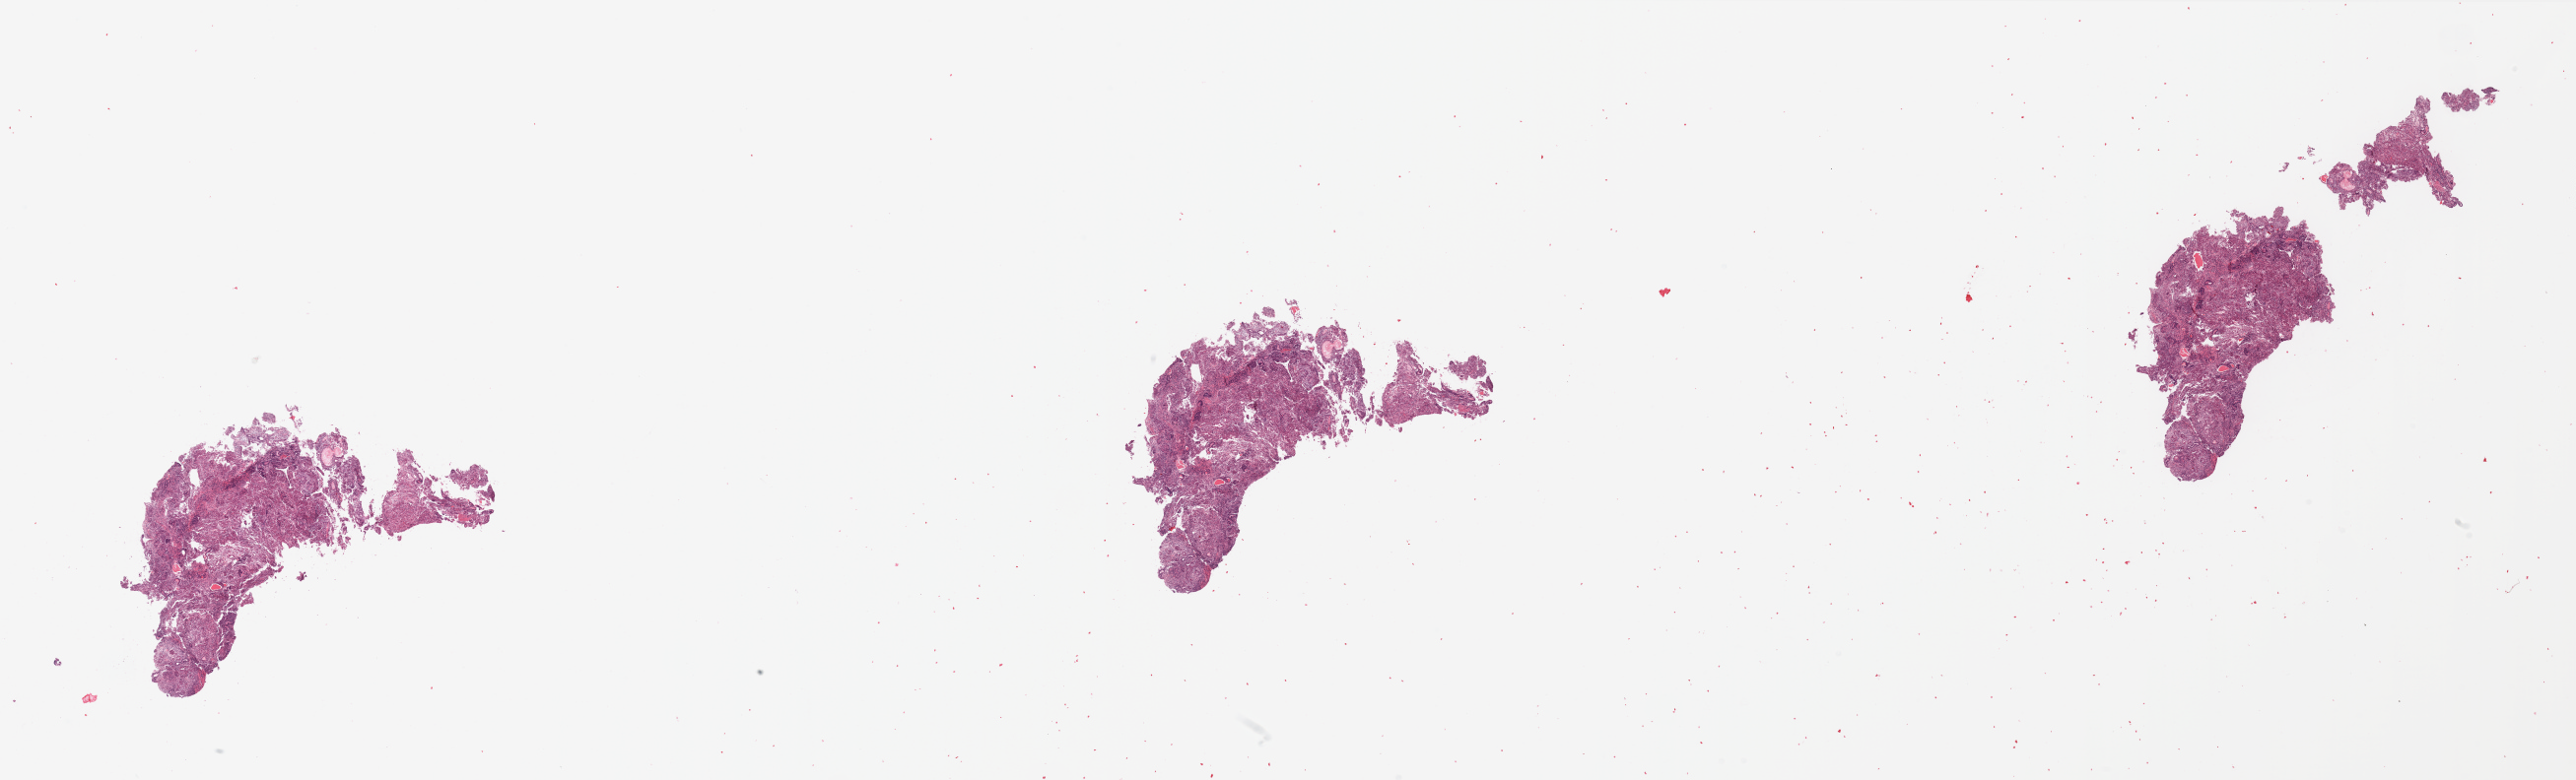
Digitized Hematoxylin and eosin (H&E) stained tissue section (whole slide) — whole scanned area (about 41.3 x 12.5 mm) shown as a low-resolution overview. Tumour tissue sample, uterus. Patient: female, age 72 years. Histologic grade: G3 (poorly differentiated).
Diagnosis: Endometrioid adenocarcinoma, NOS. AJCC pathologic stage: III.